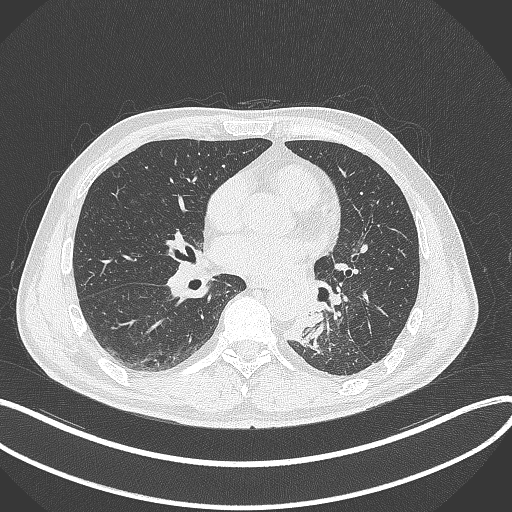
Chest CT, one axial slice; position 151 of 329 along the scan axis; reconstruction kernel B70f; lung window (W 1500 / L -600 HU); 1 mm slice thickness; 512 × 512 image matrix. Patient: male, 59 years. From the clinical record (not read from this slice): clinical TNM (as recorded): T2a N2 M0.
Annotated regions visible in this slice (rectangle marked by the reading radiologist):
- lung tumour (recorded histology: squamous cell carcinoma): bounding box (x1, y1, x2, y2) in pixels: (285, 287, 320, 345)